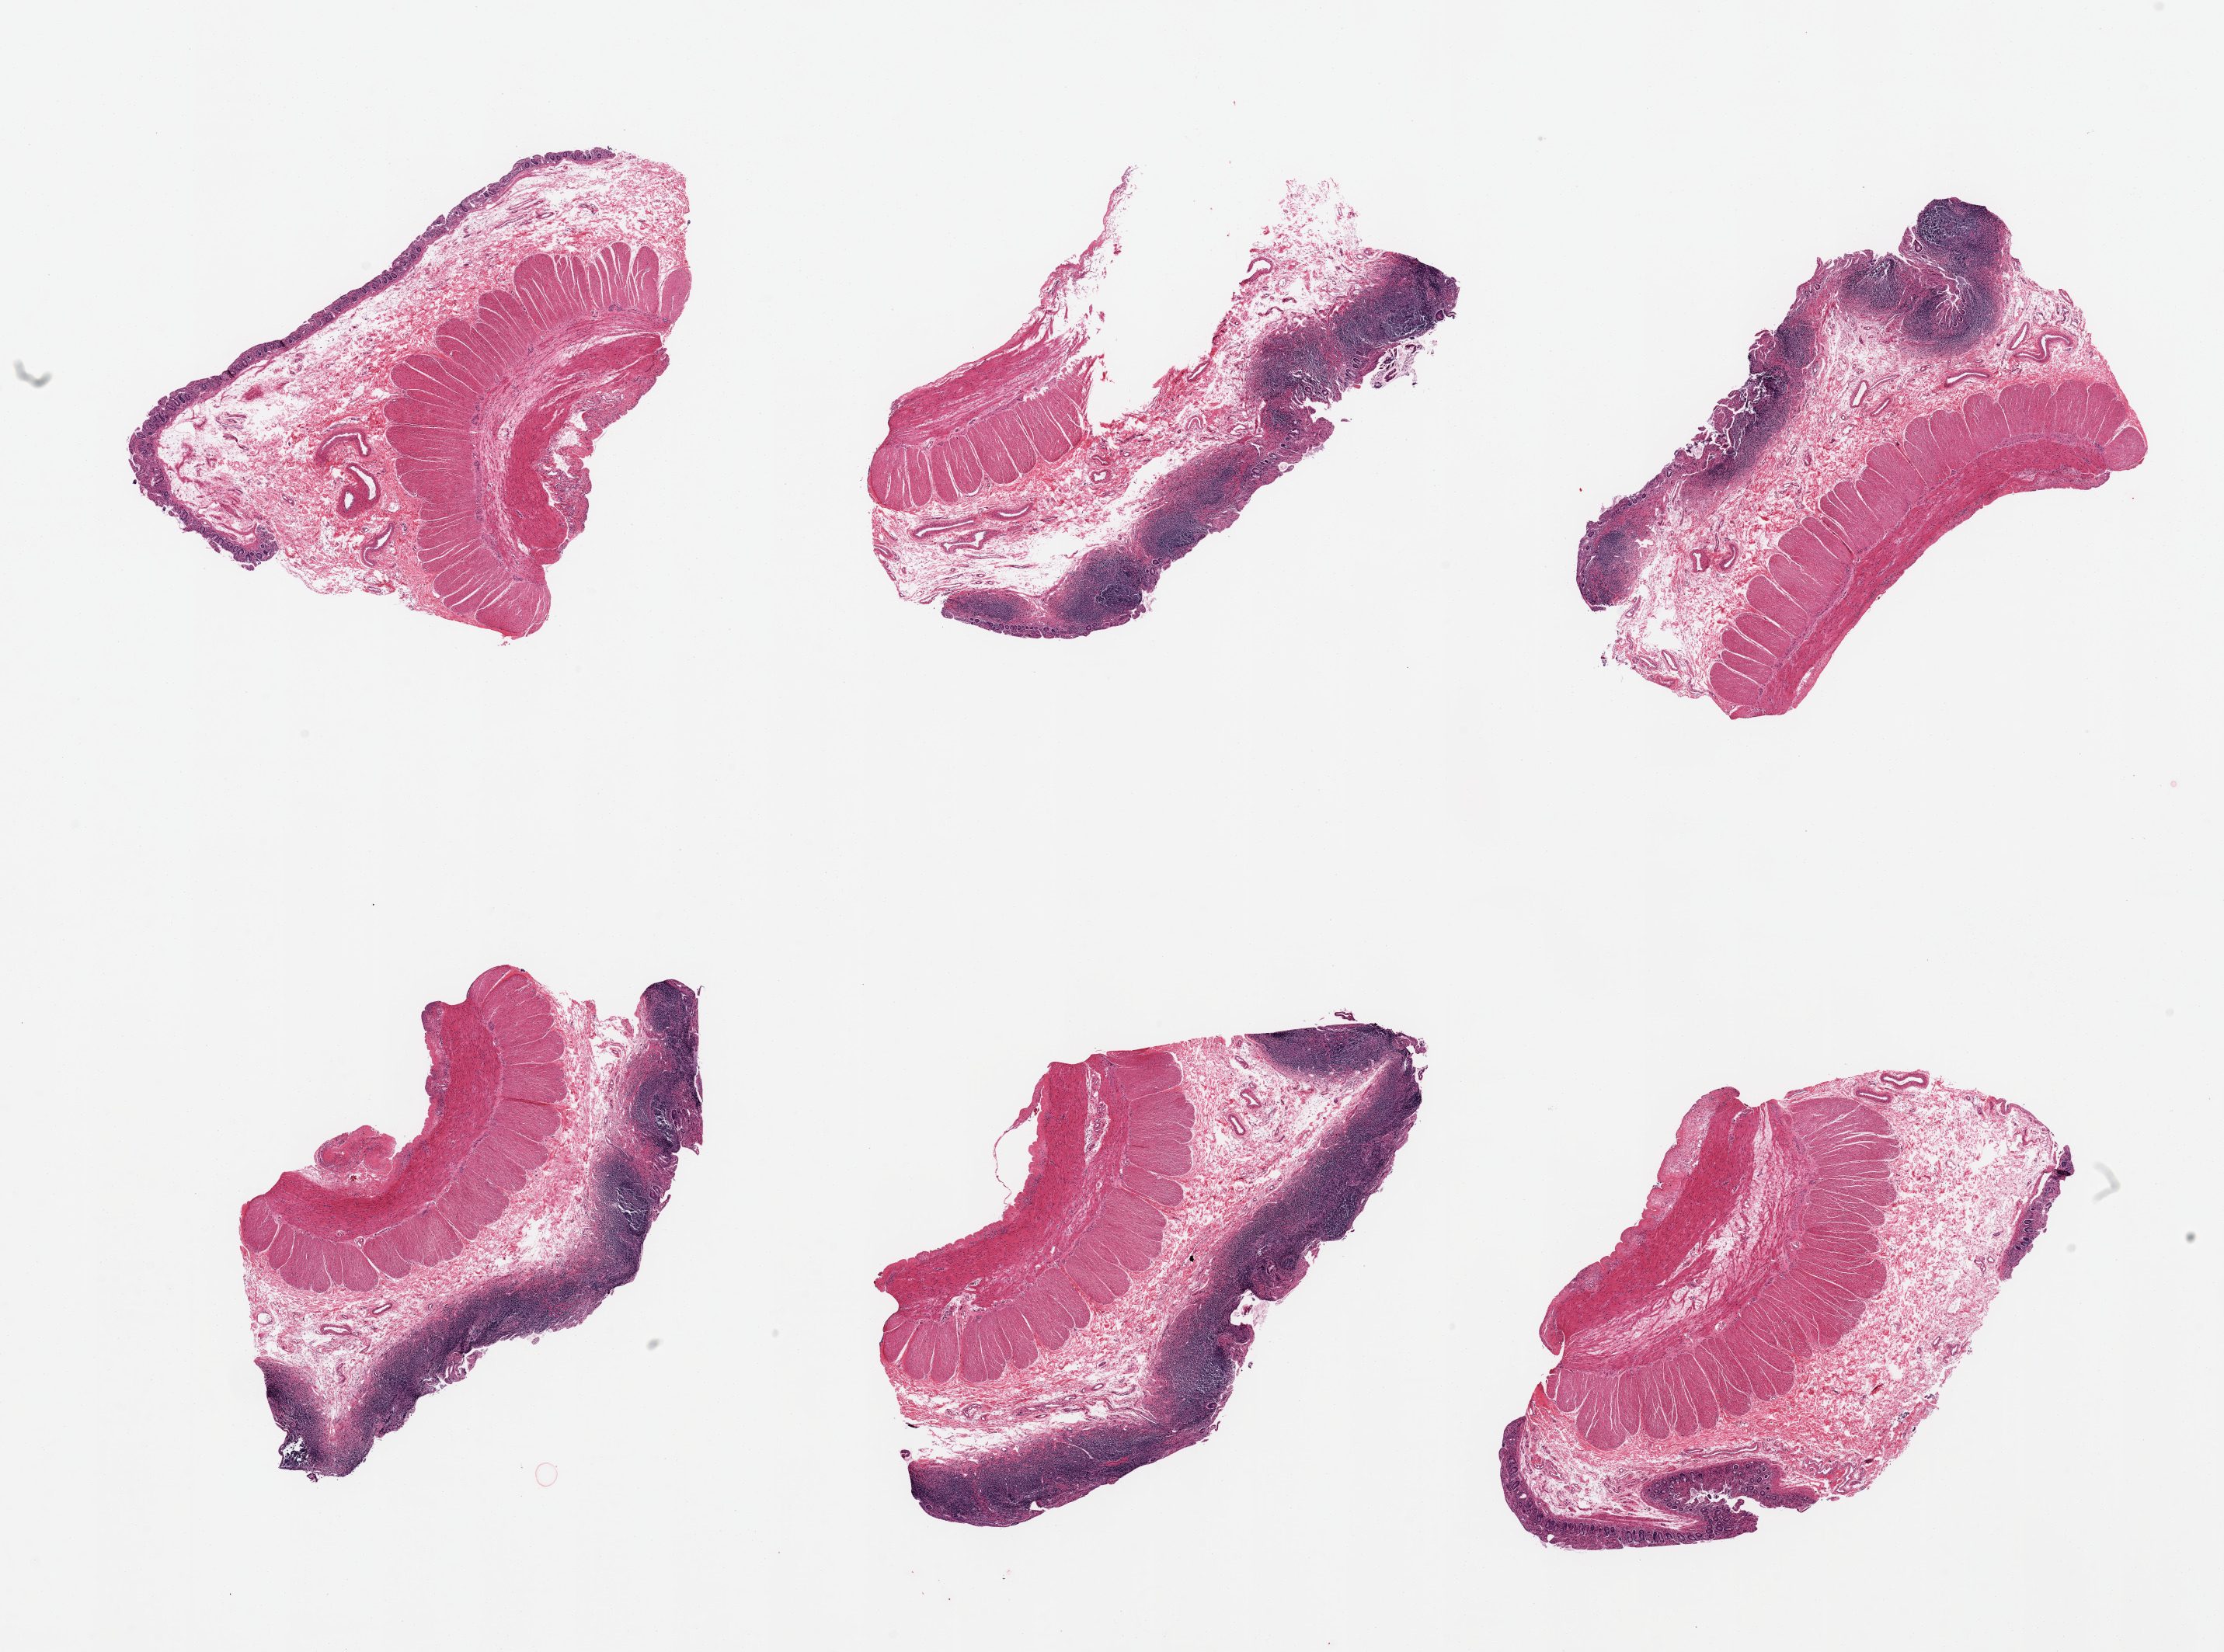
Digitized hematoxylin and eosin (H&E)-stained section, brightfield — a low-resolution overview of the entire scanned area, about 22.6 x 16.8 mm (slide scanned at 20x), PAXgene-fixed, paraffin-embedded tissue, sampled site (target tissue): ileum, tissue donor sample. Male donor.
Pathologist's review note for this sample: 6 pieces, target lymphoid aggregates are ~20% of tissue; good specimen.